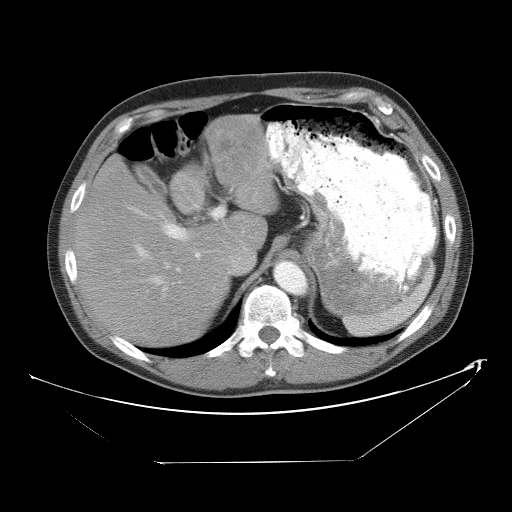
Contrast-enhanced abdominal CT, one axial slice. Slice 37 of 53 in the series (ordered by position). 120 kVp. Intravenous contrast given. Soft-tissue window (W 400 / L 40 HU). 5 mm slice thickness. 512 × 512 image matrix. Male patient, age 59 years. Case-level facts recorded for this patient, not image findings: diagnosis: colorectal cancer liver metastases, imaged before liver resection.
Annotated regions visible in this slice (outlined manually by an expert reader):
- hepatic veins: bounding box <132,244,181,292> (left, top, right, bottom; pixels)
- liver: <77,117,275,345>
- planned liver remnant (the part of the liver to remain after resection): <77,160,235,345>
- portal vein (with intrahepatic branches): <129,207,223,284>
- liver metastasis: <222,141,250,161>